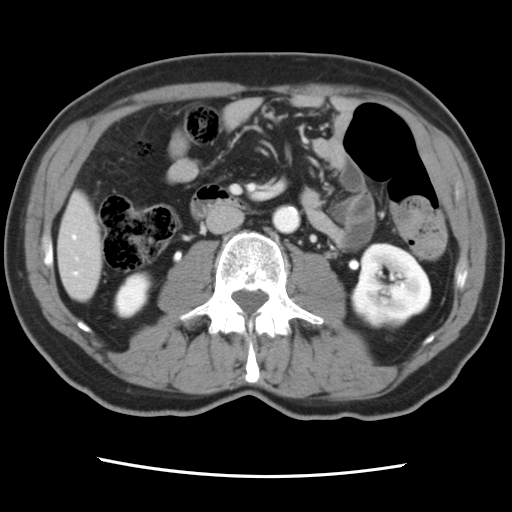
Contrast-enhanced abdominal CT, one axial slice. Position 20 of 83 along the scan axis. Intravenous contrast given. Soft-tissue window (W 400 / L 40 HU). 5 mm slice thickness. 512 × 512 image matrix, field of view 321 × 321 mm. Male patient, age 69 years. Case-level facts recorded for this patient, not image findings: diagnosis: colorectal cancer liver metastases, imaged before liver resection; multiple liver metastases: yes; largest metastasis: 3.5 cm; disease in both lobes: no.
Outlined on this slice (expert manual segmentation):
- hepatic veins: bounding box [x1, y1, x2, y2] px = [73, 236, 77, 275]
- liver: [59, 196, 104, 300]
- planned liver remnant (the part of the liver to remain after resection): [59, 195, 104, 300]